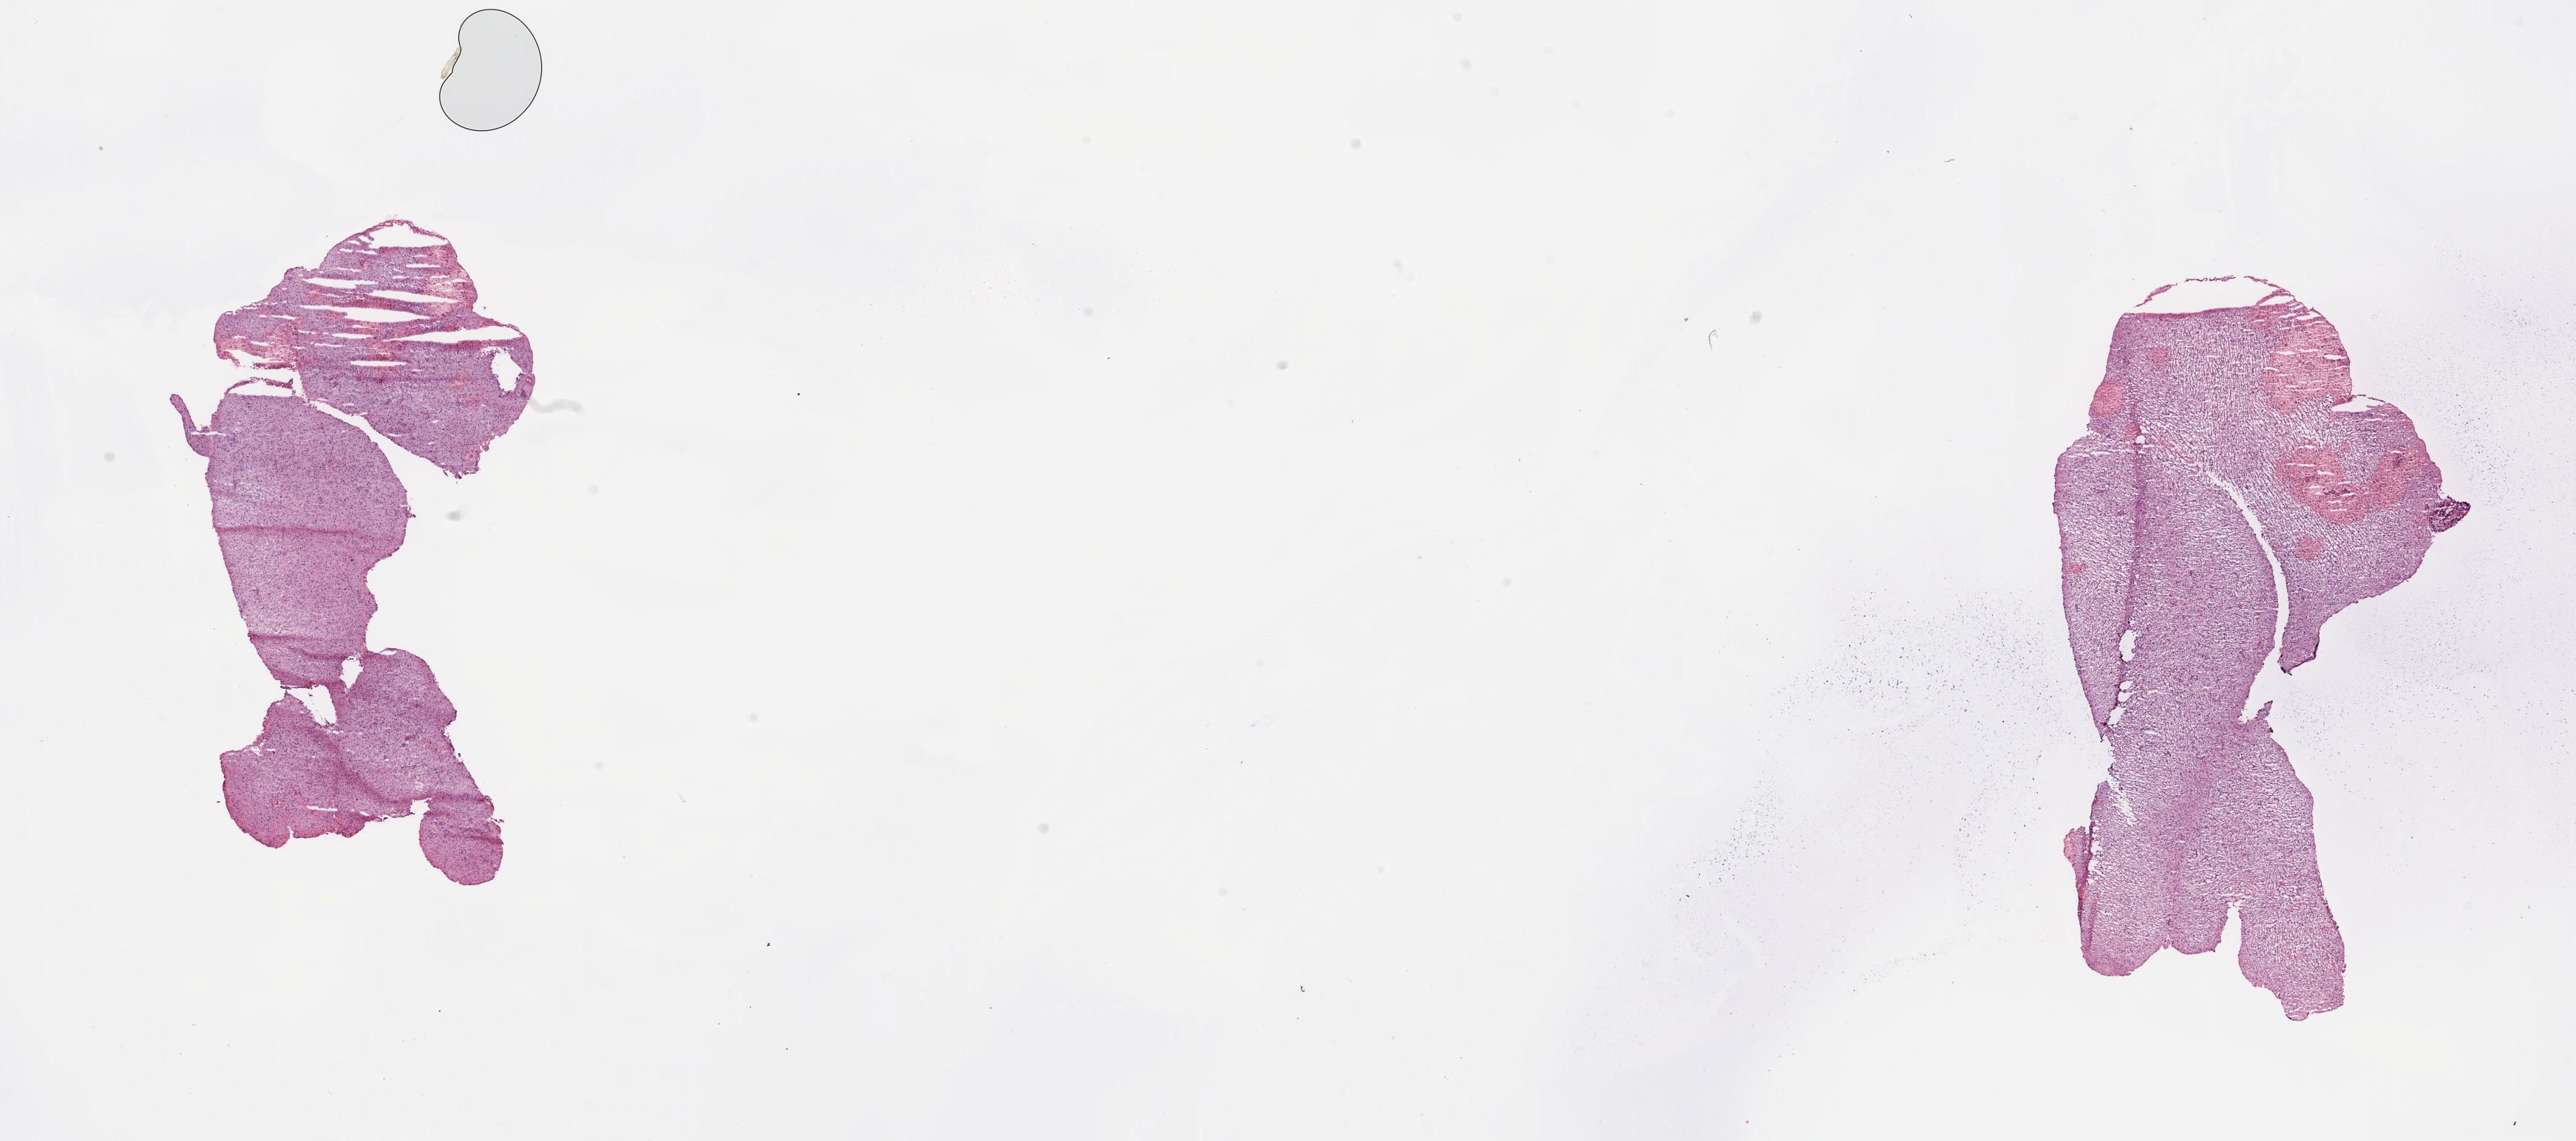
Digitized Hematoxylin and eosin (H&E) stained tissue section (whole slide) — whole scanned area (about 27.6 x 12.2 mm, acquisition: 20x scan) shown as a low-resolution overview, tumour tissue sample, brain. 77-year-old male patient.
Primary tumour site (as recorded): parietal lobe. Patient diagnosis (cohort enrolment): glioblastoma multiforme (brain).